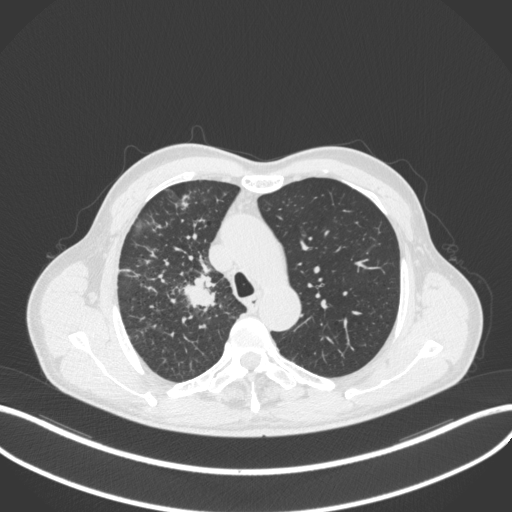
Chest CT, one axial slice. Position 353 of 490 along the scan axis. 120 kVp. Lung window (W 1500 / L -600 HU). 1 mm slice thickness. 512 × 512 image matrix, field of view 400 × 400 mm. Male patient, age 69 years. From the clinical record (not read from this slice): clinical TNM (as recorded): T2a N0 M0.
Annotated regions visible in this slice (rectangle marked by the reading radiologist):
- lung tumour (recorded histology: adenocarcinoma): box from (x=177, y=270) to (x=222, y=318) px